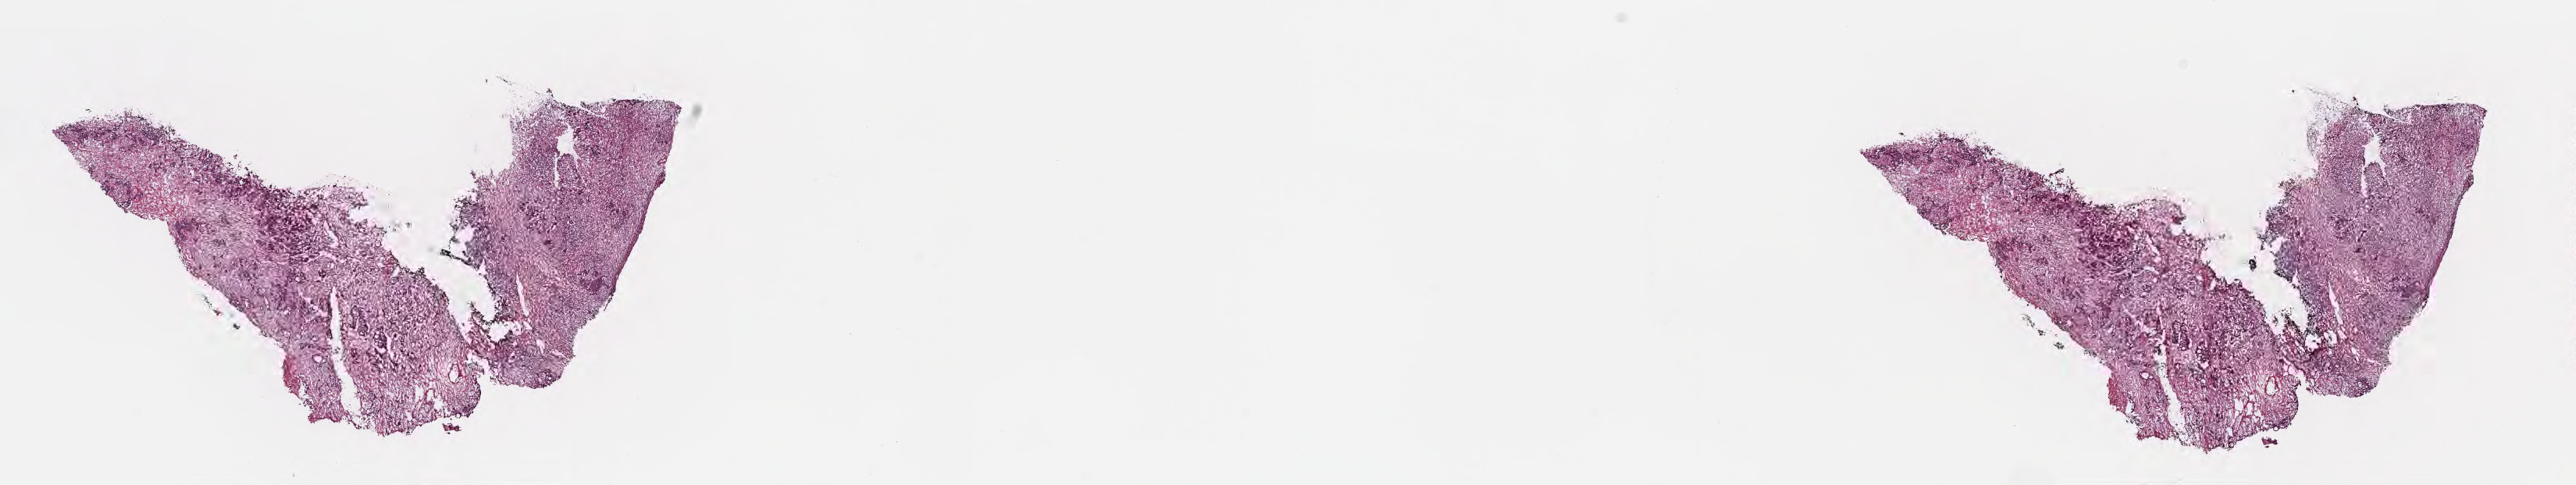
Hematoxylin and eosin (H&E) whole-slide image — a low-resolution overview of the entire scanned area, about 26.7 x 5.0 mm. Frozen section (tissue freezing medium). Metastatic tumor tissue, resected from lymph node. Male patient; age at initial diagnosis 56 years. Pathologist review of this section (percent, as recorded): tumor cells 40%, tumor nuclei 50%, stromal cells 60%, necrosis 0%, normal cells 0%. Infiltration values recorded for this section: lymphocyte infiltration 0%, monocyte infiltration 0%, neutrophil infiltration 0%.
Patient diagnosis (primary): Adenocarcinoma, metastatic, NOS.